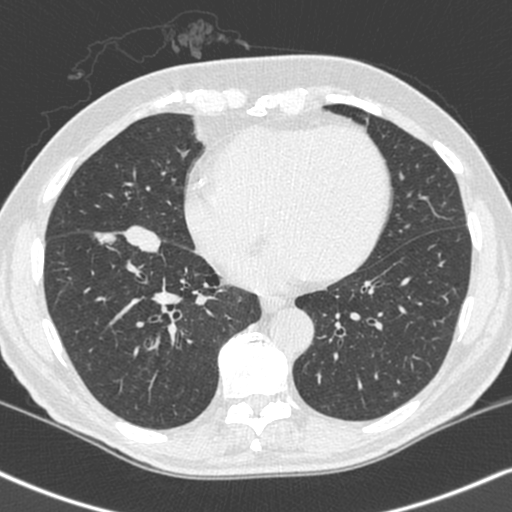
Axial slice from a low-dose chest CT screening exam; baseline screening round; lung window (W 1500 / L -600 HU); 1.3 mm slice thickness; standard (soft-tissue) reconstruction kernel (C); 120 kVp. Male, age 68 years at enrolment. Current smoker at enrolment.
Expert-annotated lung lesion, box from (x=87, y=223) to (x=162, y=294) px. The exam's reader record, not a measurement of the box and not confirmed to be the same lesion: non-calcified nodule or mass ≥4 mm, right lower lobe, 34 × 17 mm, smooth margins, soft tissue attenuation. Official screen result: positive, change unspecified: nodule(s) >= 4 mm or enlarging nodule(s), mass(es), or other non-specific abnormalities suspicious for lung cancer. Participant outcome: lung cancer diagnosed 24 days after this screen — combined small cell carcinoma, right lower lobe, stage IIIA (AJCC 6th edition), 41 mm at pathology.